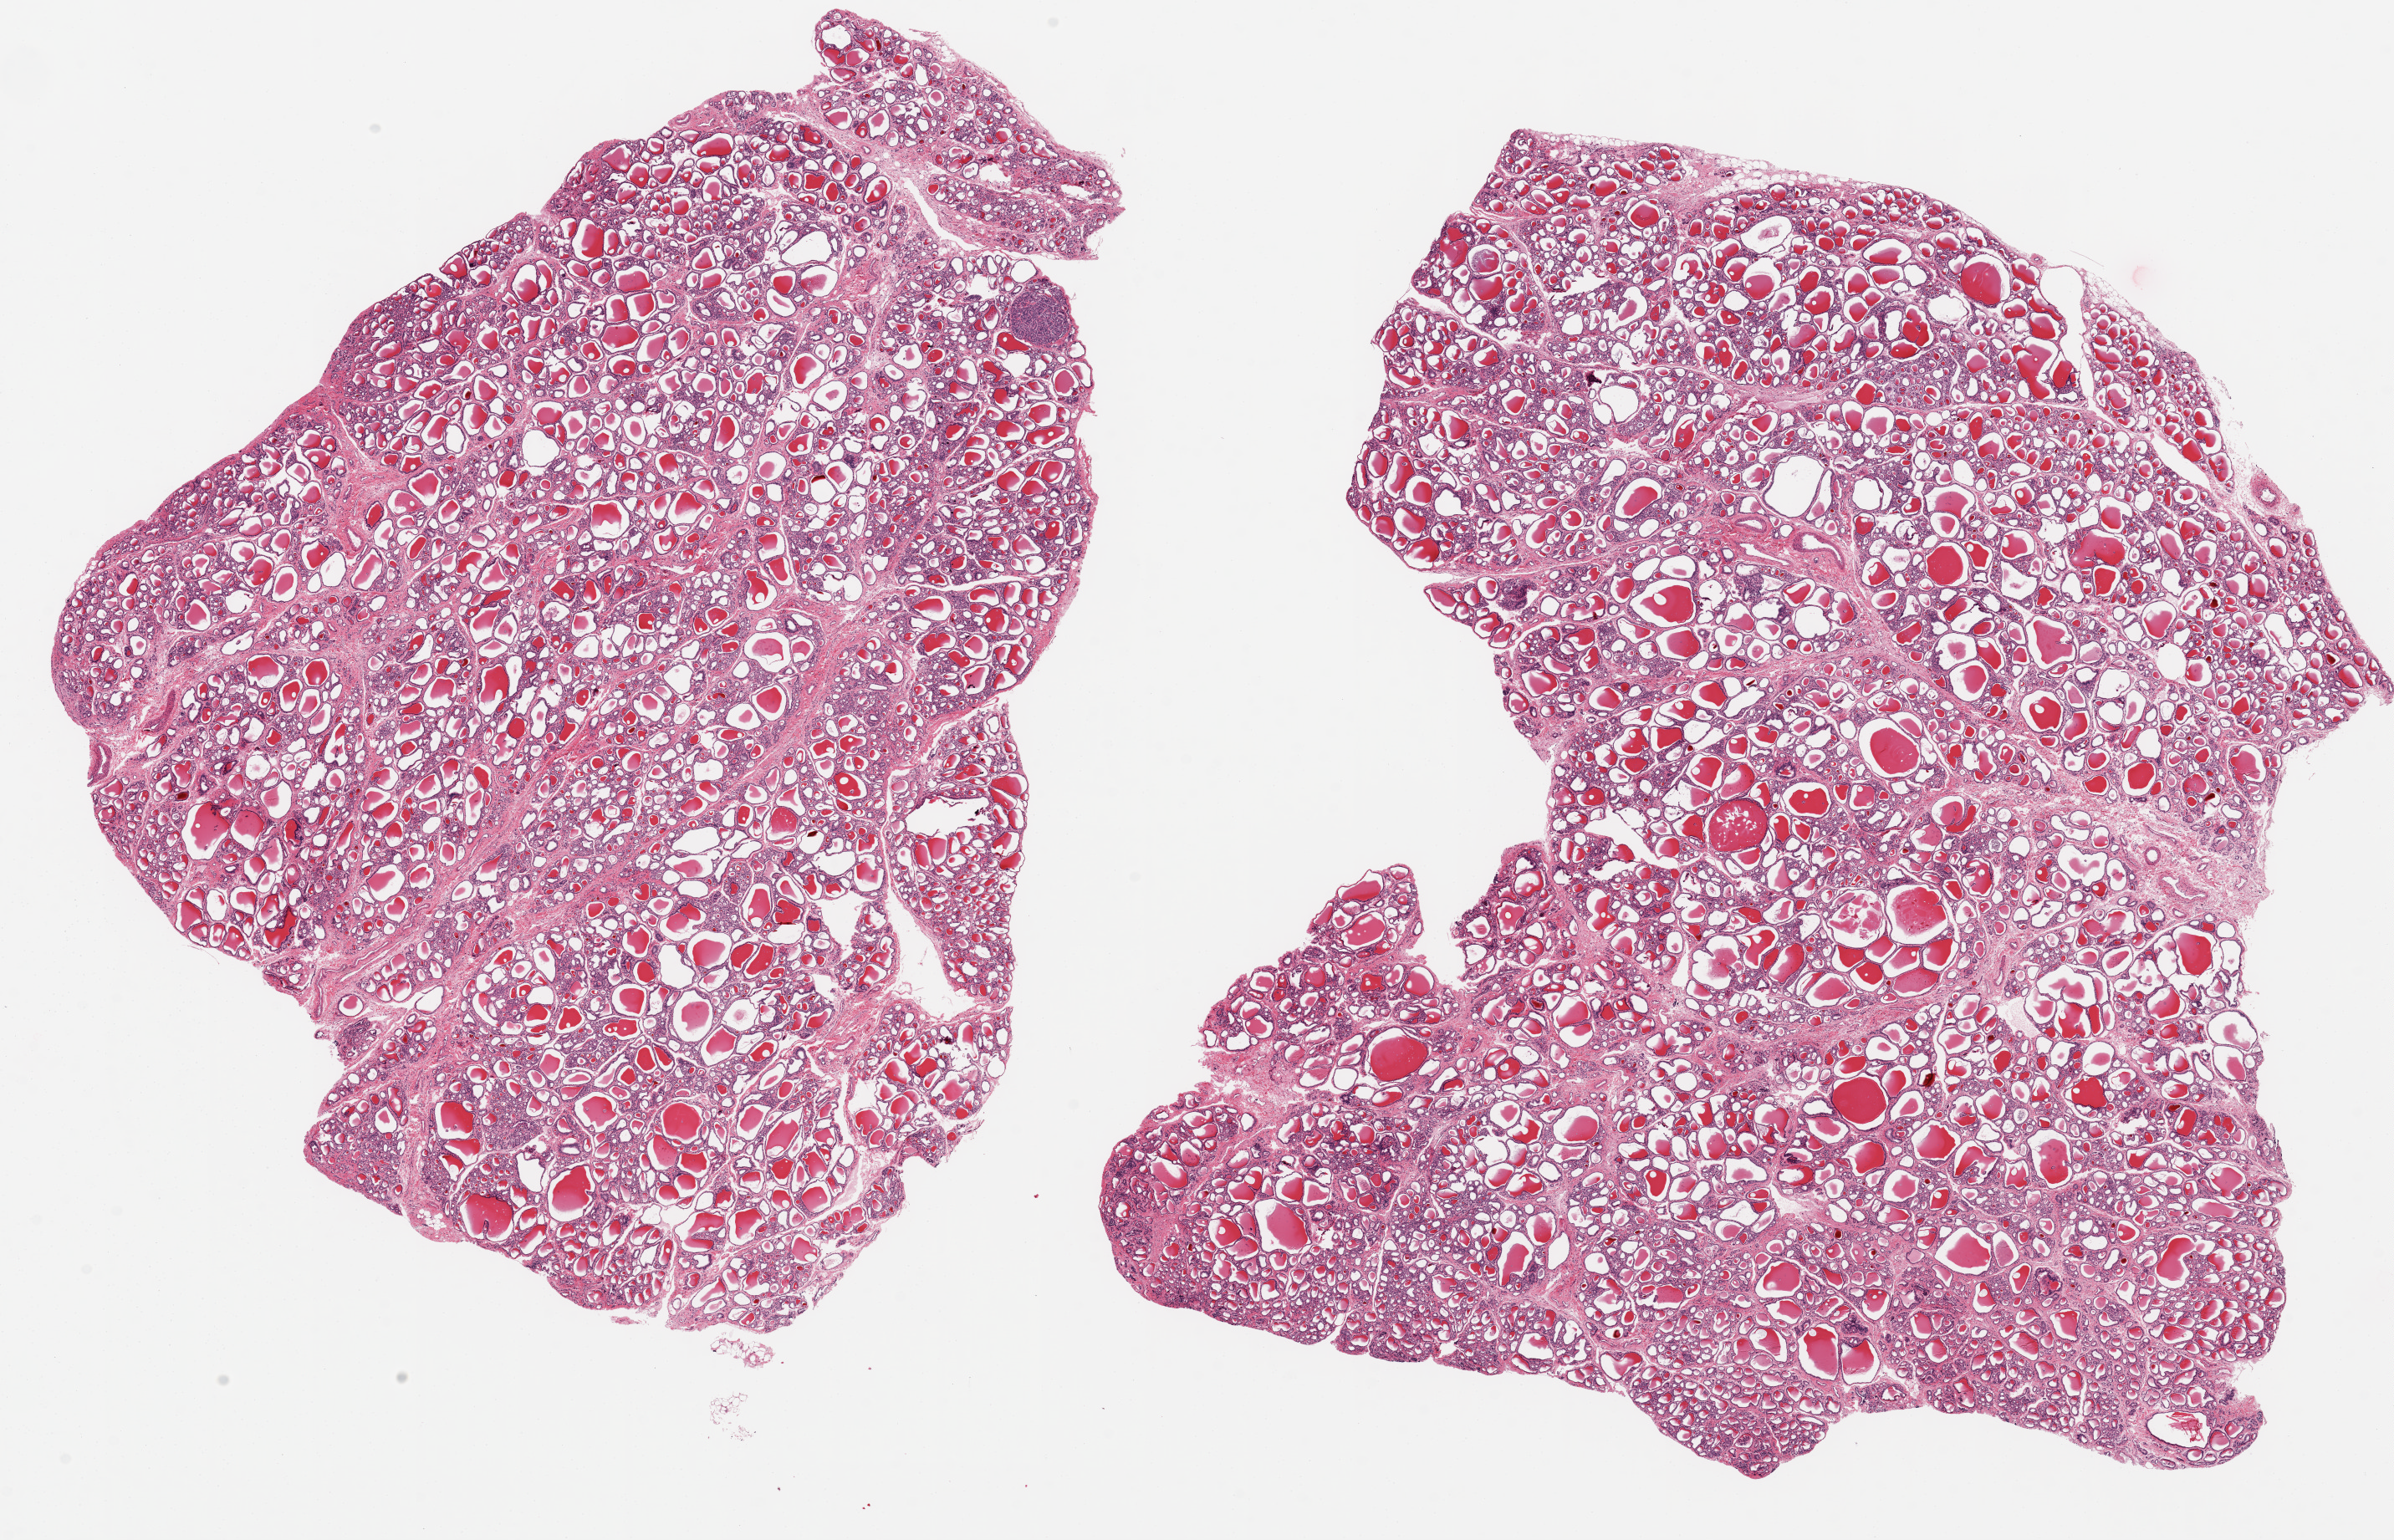
Hematoxylin and eosin (H&E) whole-slide image, whole scanned area (about 22.6 x 14.6 mm, slide scanned at 20x) shown as a low-resolution overview; PAXgene-fixed paraffin-embedded (PFPE) section; target tissue: thyroid; tissue donor sample. Donor: male.
Reviewer comment on this tissue sample: 2 ~12x10mm aliquots, one with incidental 0.5mm adenoma.